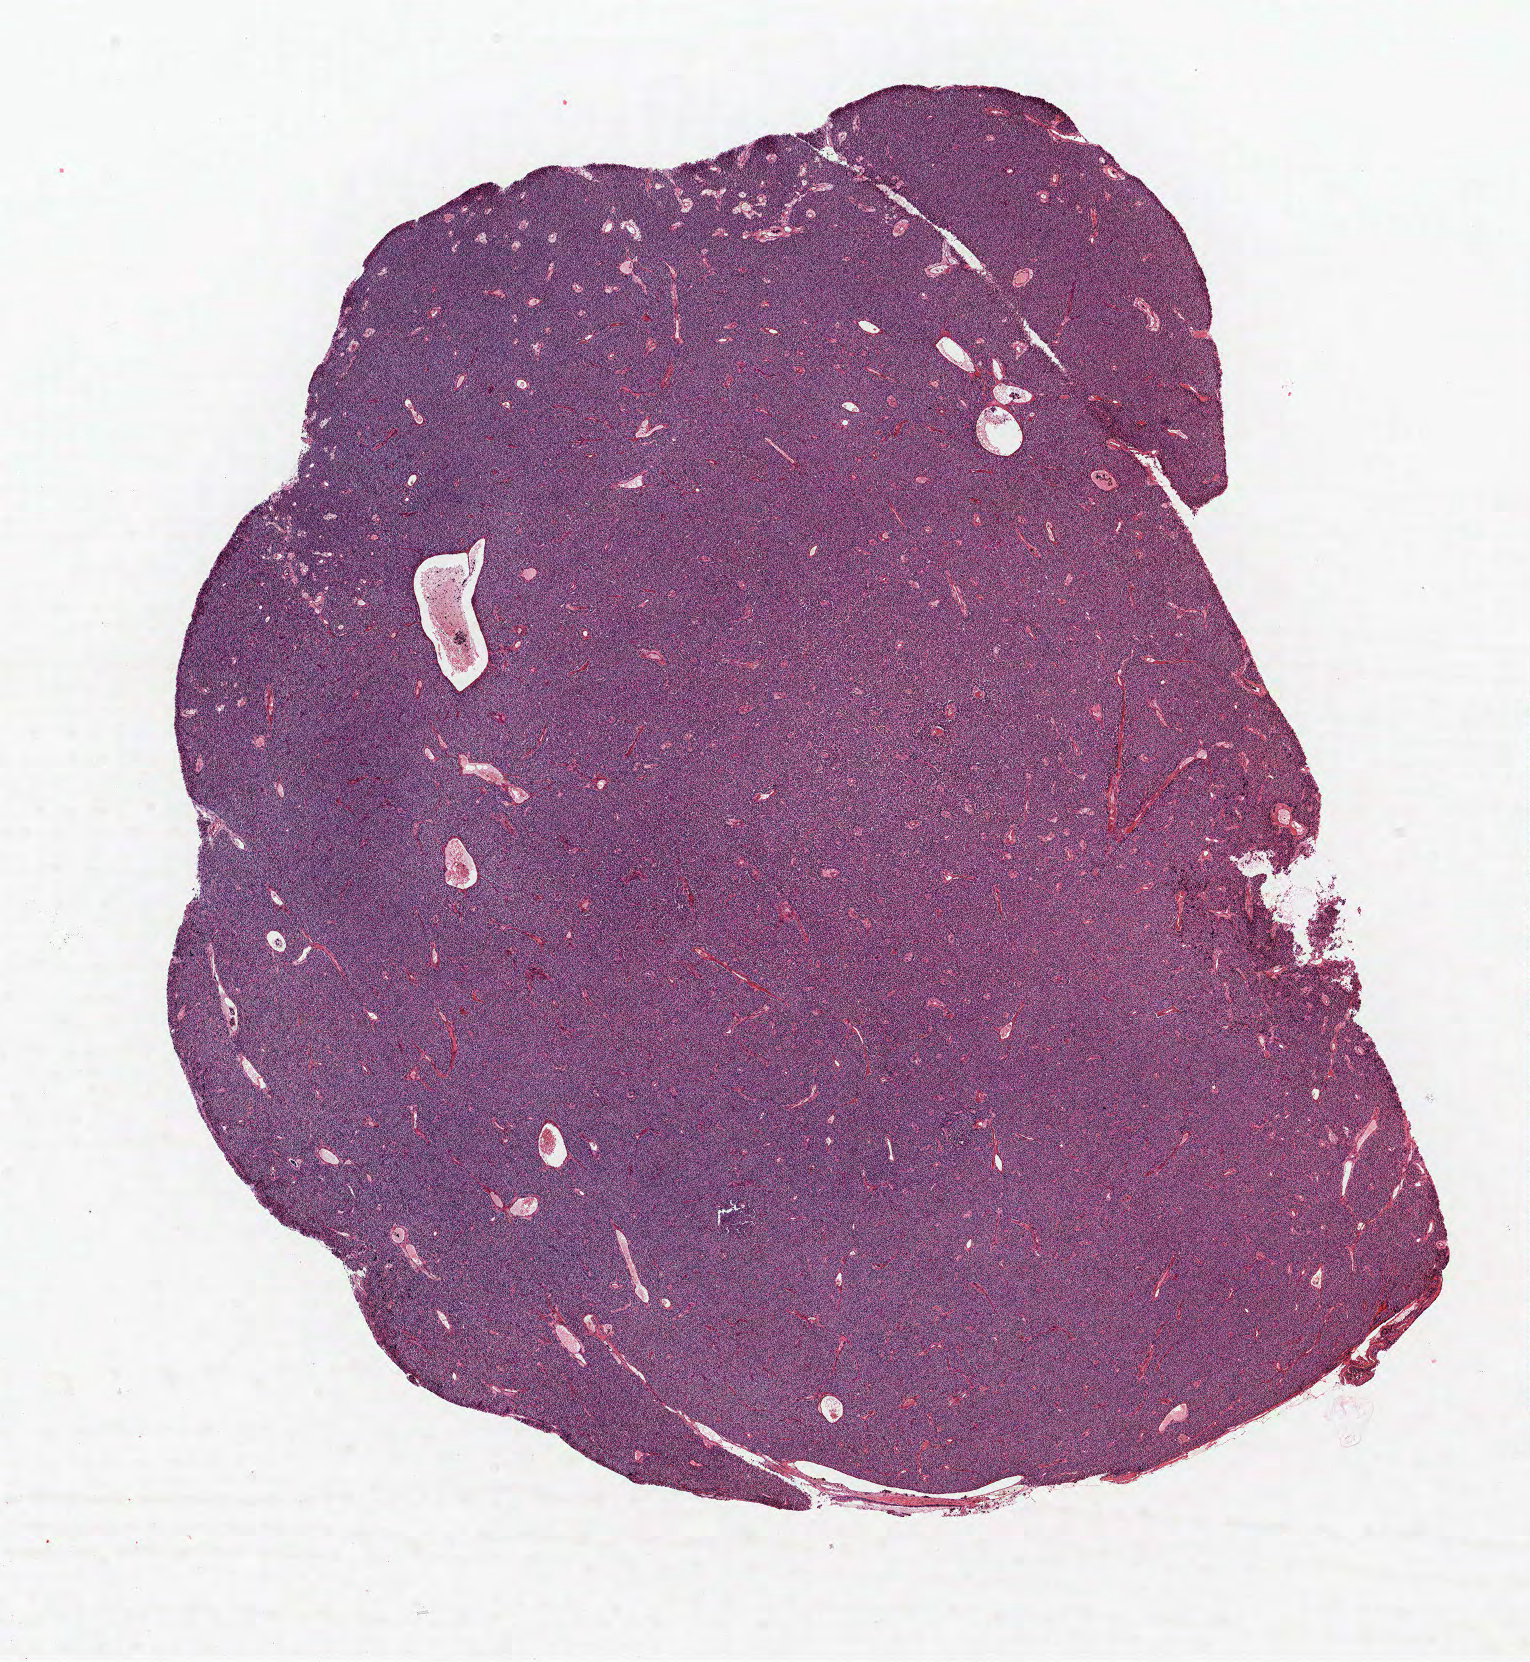
Whole-slide histology image, Hematoxylin and eosin (H&E) stained, shown as a low-resolution overview of the whole scanned area (about 12.2 x 13.3 mm, from a 40x scan); formalin-fixed paraffin-embedded (FFPE) section; lung tissue. Female, age 55 at enrolment.
Stage (AJCC 7th edition): IA. Participant's lung-cancer diagnosis: Carcinoid tumor, NOS (ICD-O-3 8240/3). Primary tumour location (clinical record): left lower lobe. Tumour size (pathology): 10 mm. ICD-O-3 topography: lower lobe of lung (C34.3).